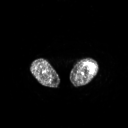
FDG PET of an extremity soft-tissue mass (from a PET/CT study), one axial slice; position 194 of 267 along the scan axis; 3.27 mm slice thickness; 128 × 128 image matrix, field of view 700 × 700 mm. Female patient, age 62 years. Case-level facts recorded for this patient, not image findings: histological type: undifferentiated – high grade; grade: high; site of the primary tumour: left thigh.
Annotated regions visible in this slice (expert contour drawn on MRI and transferred to this co-registered scan by the dataset authors):
- gross tumour volume including surrounding oedema: bounding box (x1, y1, x2, y2) in pixels: (85, 63, 95, 72)